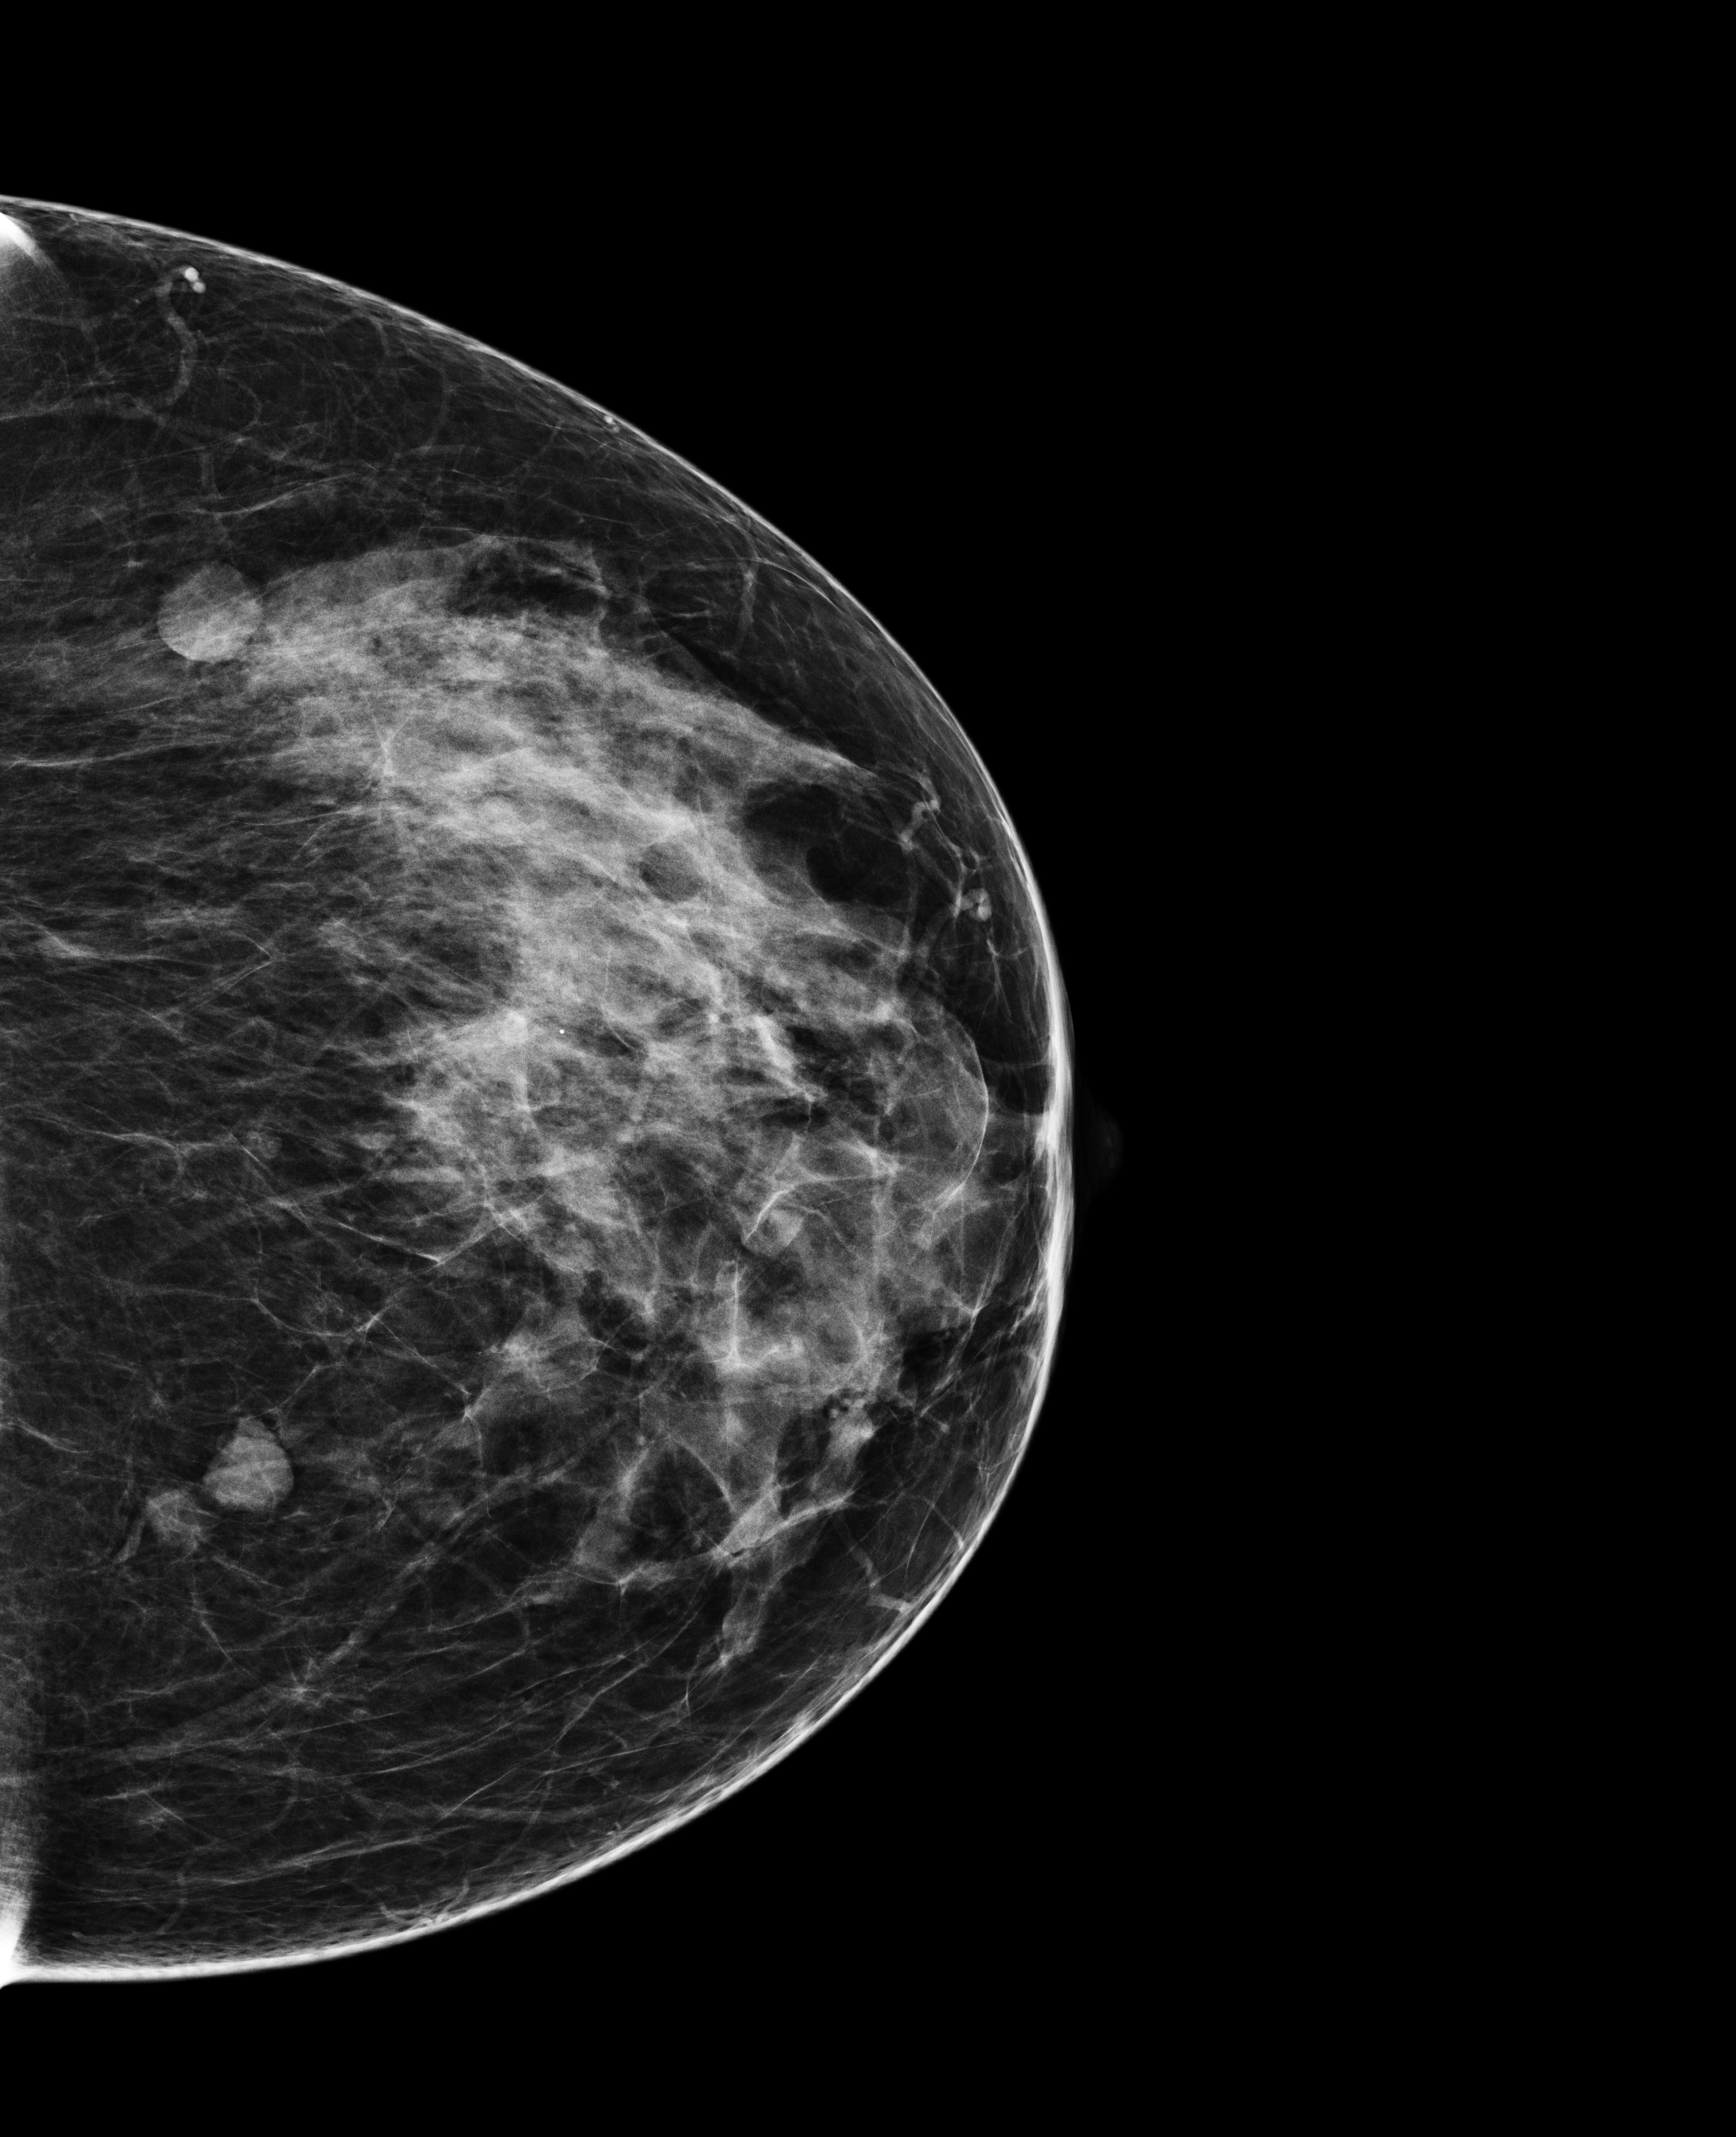
Digital mammogram (FFDM), left breast, CC view, screening examination. Patient aged 48 years (female).
Final BI-RADS category for the screening round (tomosynthesis exam, both breasts): category 2.